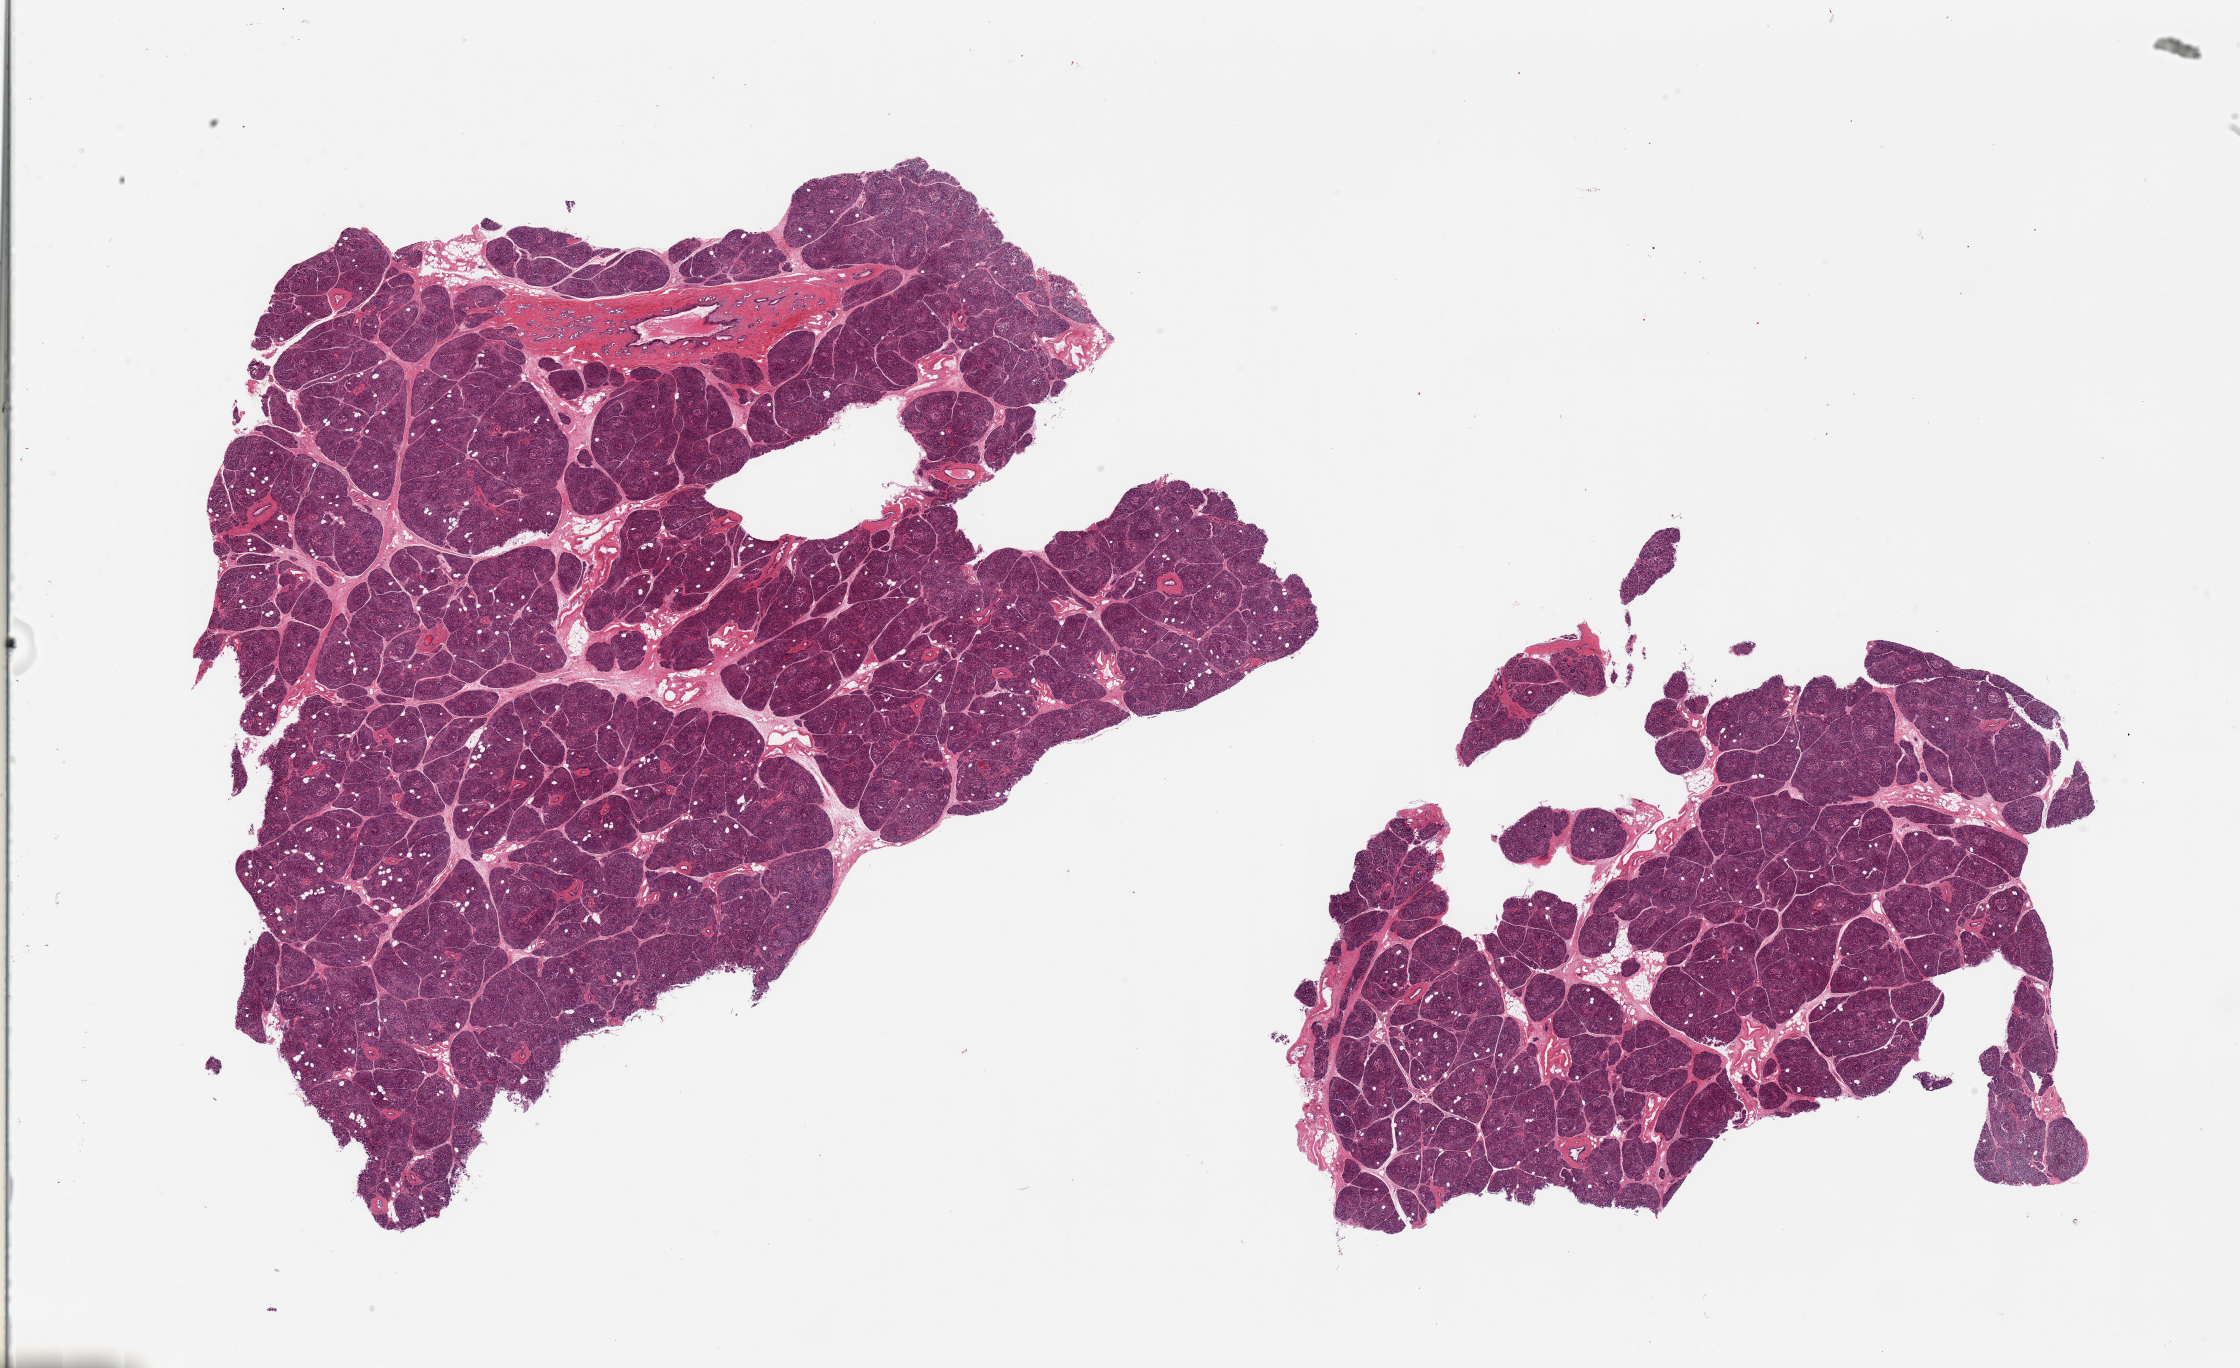
Digitized haematoxylin and eosin-stained section, shown as a low-resolution overview of the whole scanned area (about 35.4 x 21.6 mm, from a 20x scan), PAXgene-fixed, paraffin-embedded tissue, section of pancreas (target tissue), donor tissue sample. Donor sex: female.
- pathologist's review note for this sample: 2 pieces